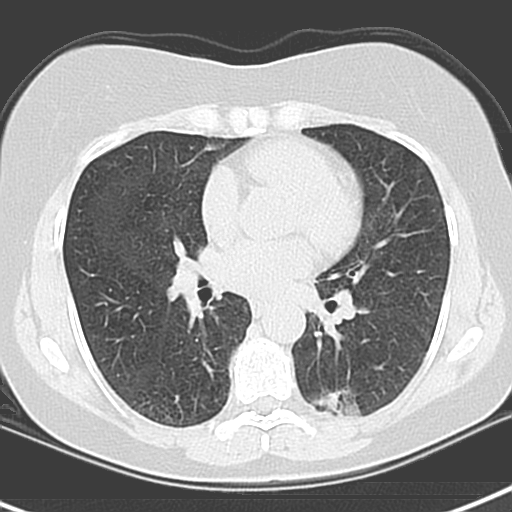
Axial slice from a low-dose chest CT screening exam. First (baseline) screen. Lung window (W 1500 / L -600 HU). 3.2 mm slice thickness. Female participant, aged 55 years at enrolment. Current smoker at enrolment.
Expert reader's lesion annotation, bounding box <310,374,387,424> (left, top, right, bottom; pixels). The screening reader recorded 3 non-calcified nodules or masses ≥4 mm on this exam (left upper lobe, left lower lobe, left lower lobe); which of them this box marks is not recorded. Official screen result: positive, change unspecified: nodule(s) >= 4 mm or enlarging nodule(s), mass(es), or other non-specific abnormalities suspicious for lung cancer. Lung cancer was diagnosed 1063 days after this screen (after the third annual screen): adenocarcinoma with mixed subtypes, left lower lobe, poorly differentiated (G3), stage IA (AJCC 6th edition), 21 mm at pathology.